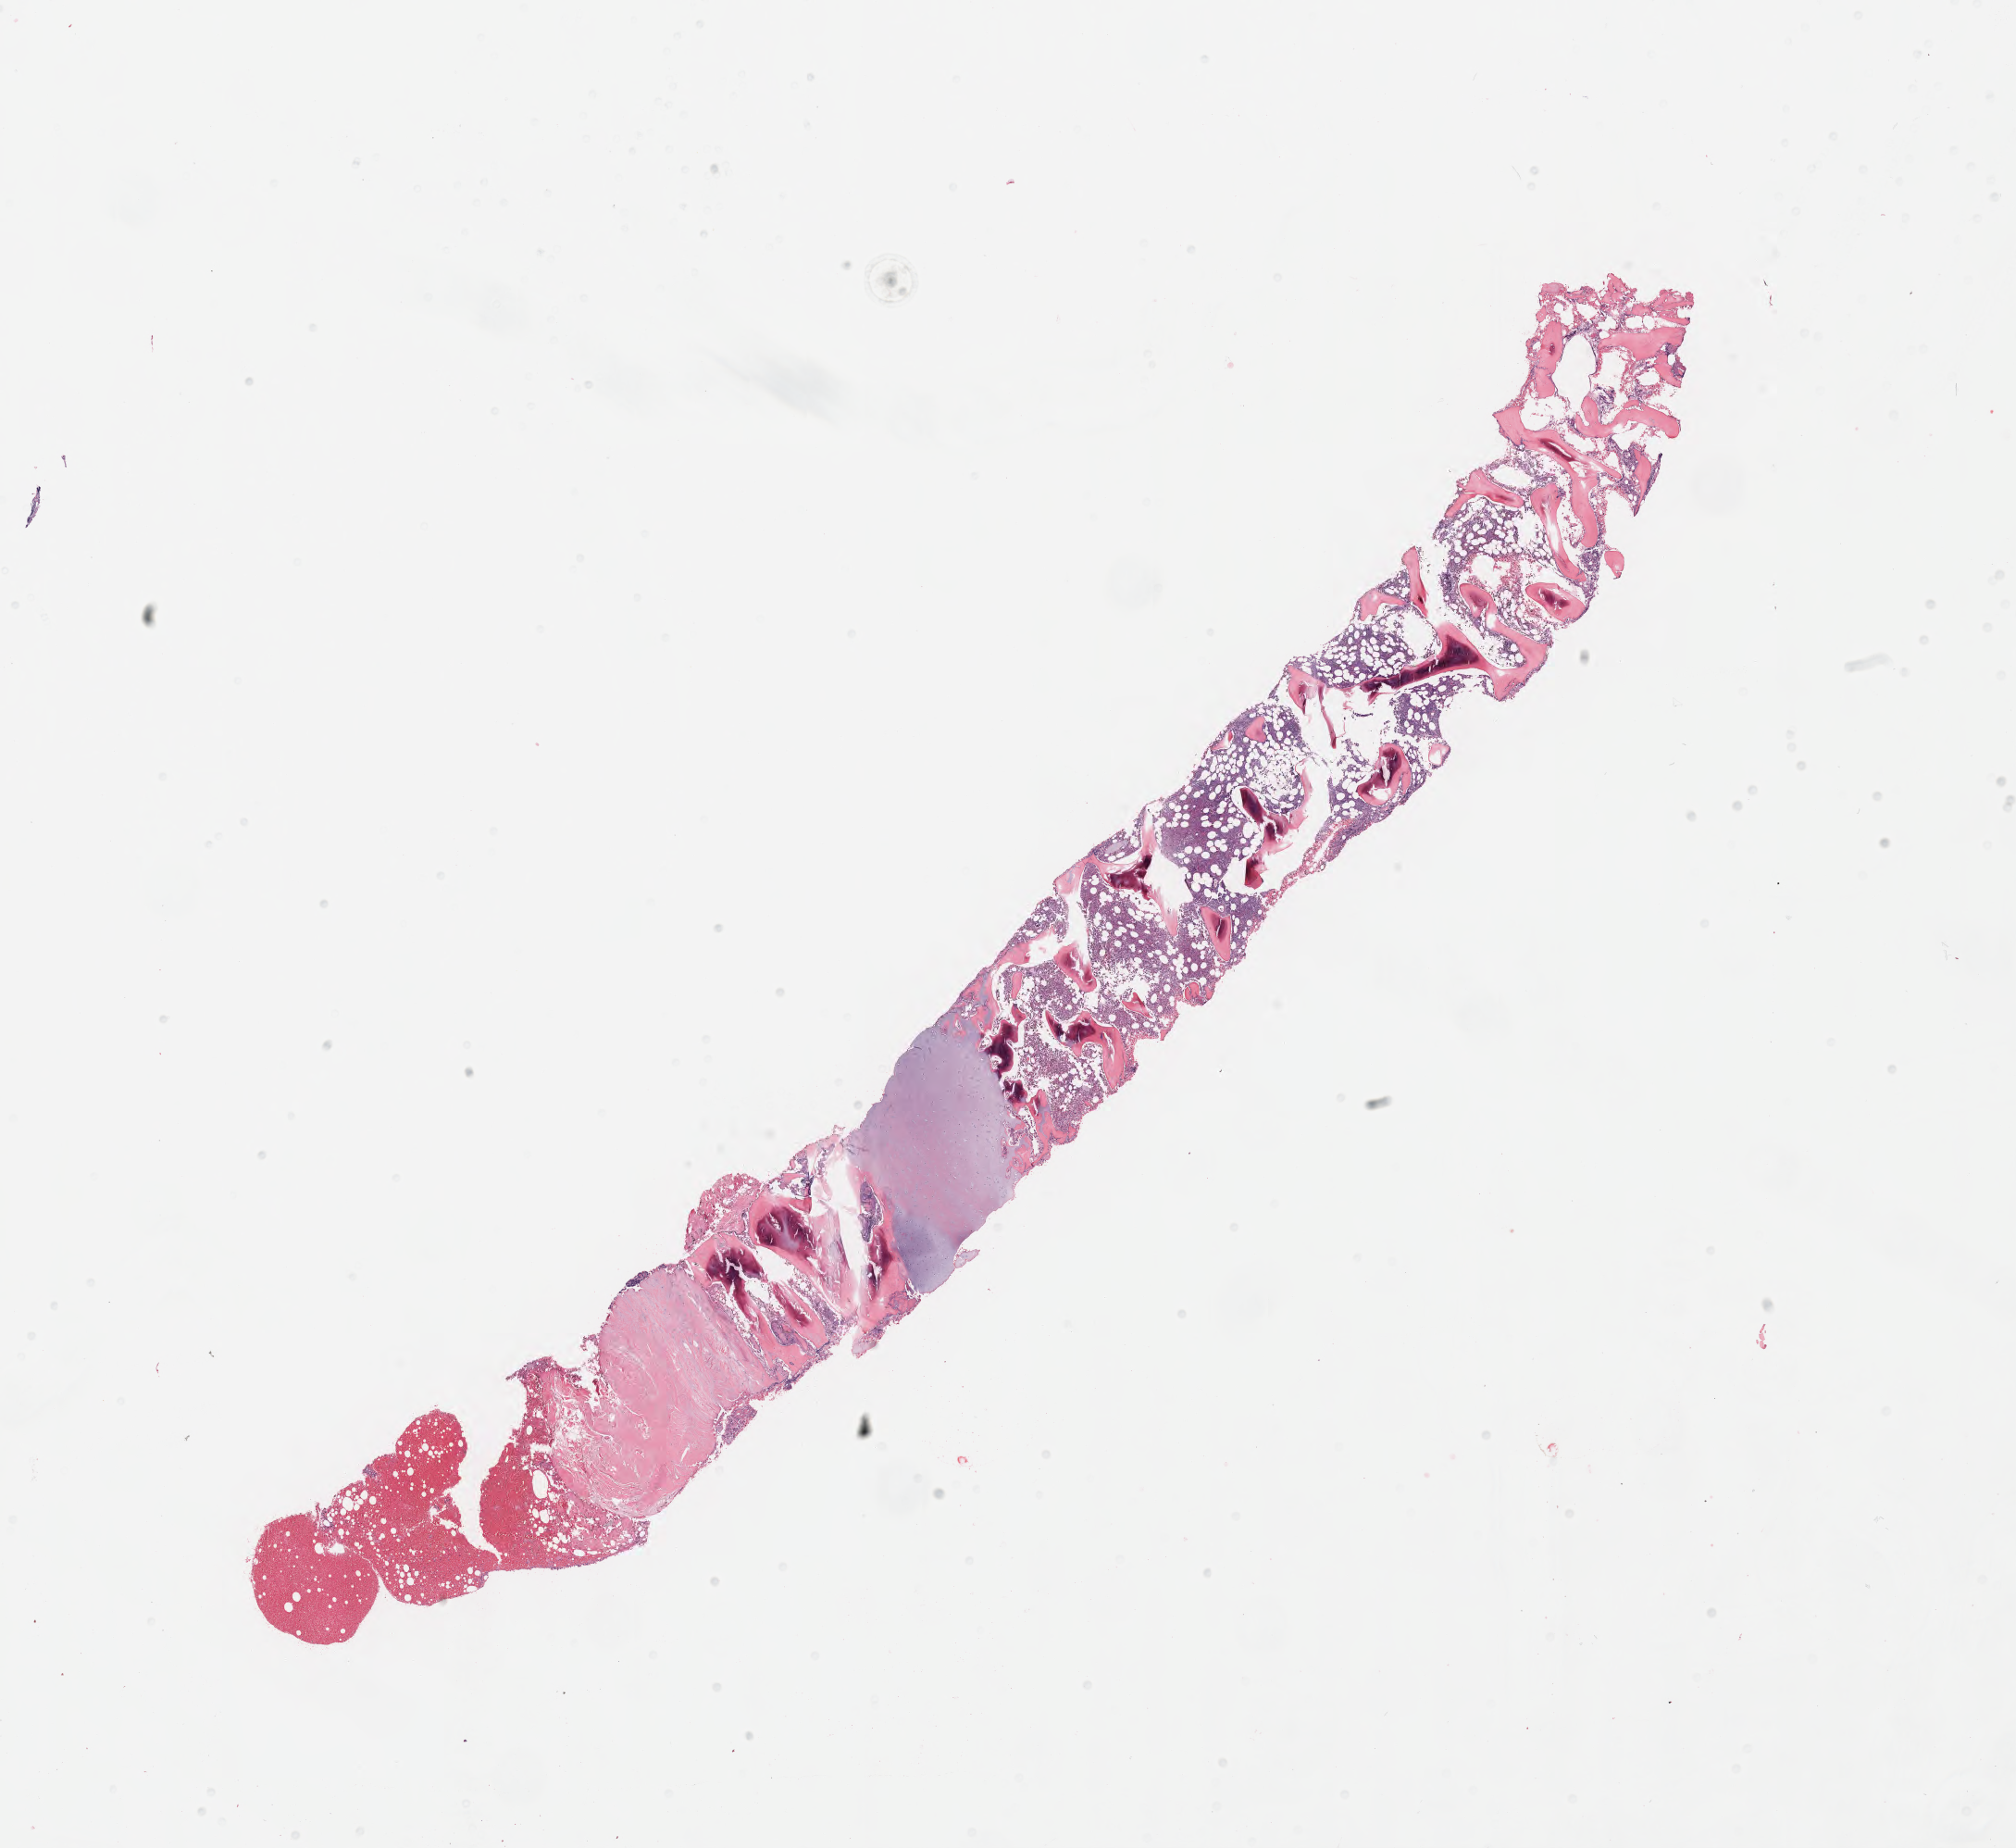
H&E whole-slide image — a low-resolution overview of the entire scanned area, about 17.6 x 16.1 mm, tumor tissue, site: bone marrow. Male patient, age 15 years.
Histologic diagnosis: Burkitt lymphoma, NOS.